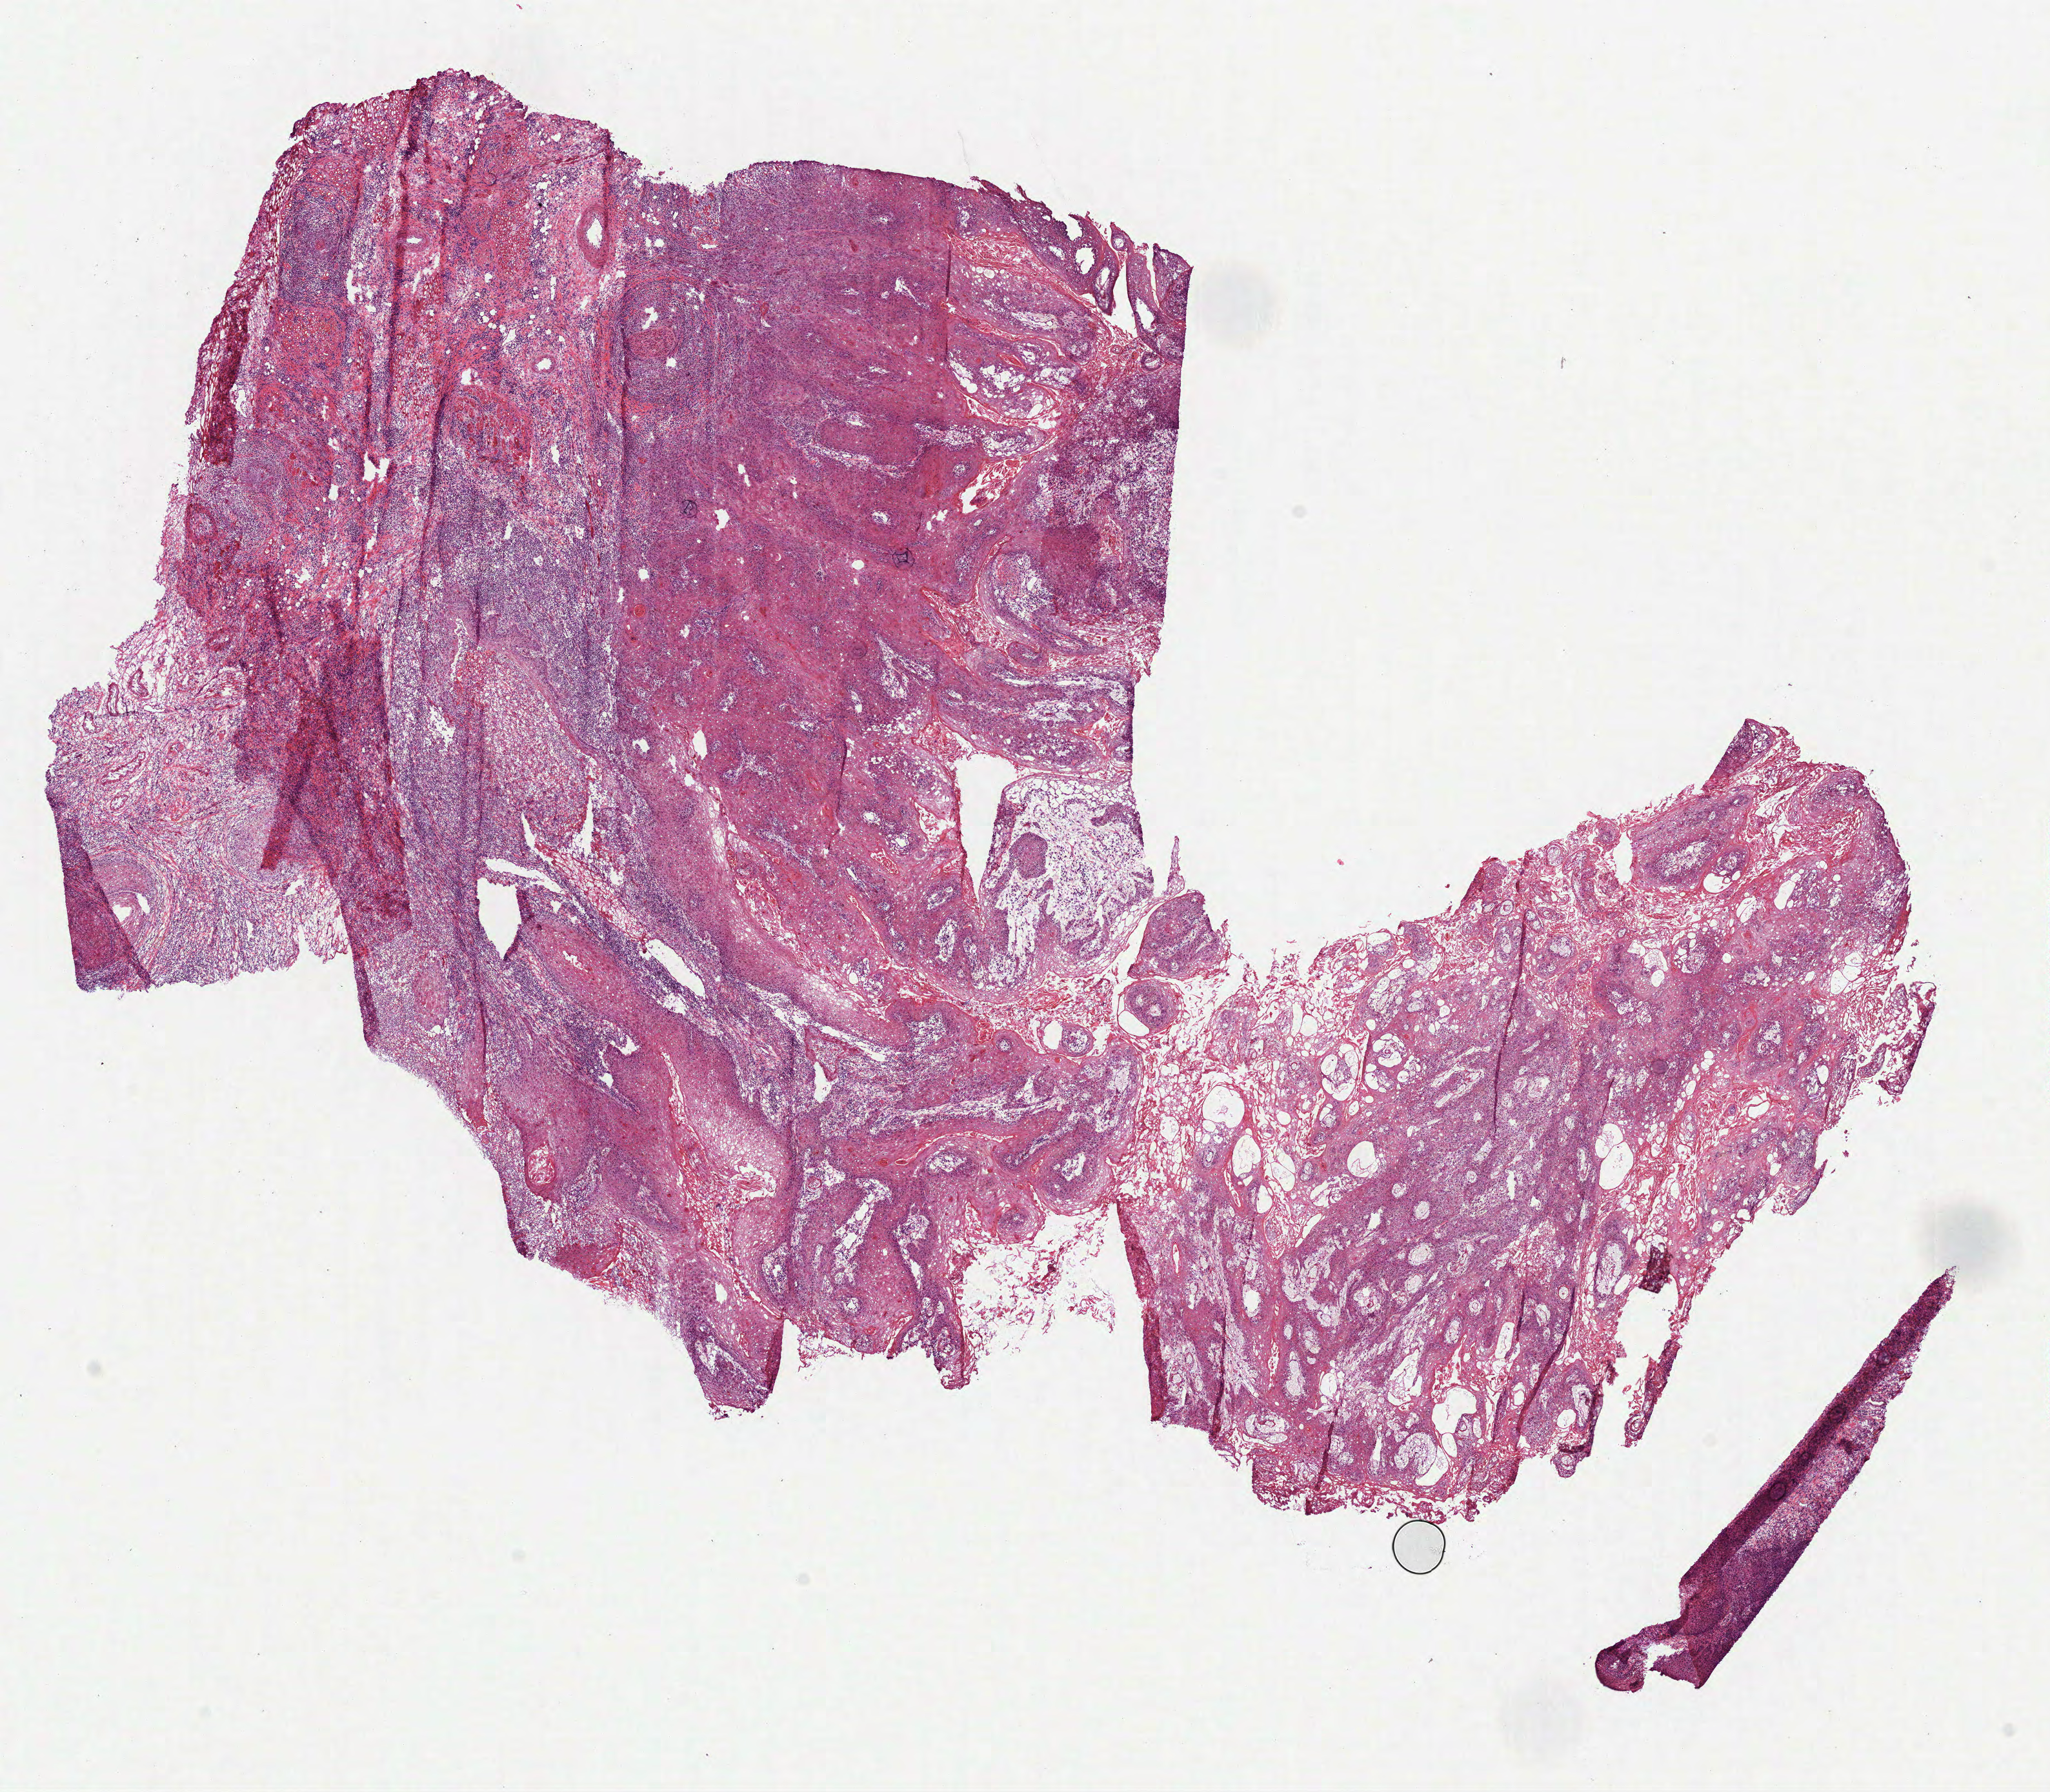
Whole-slide histology image, H&E, whole scanned area (about 12.8 x 11.2 mm, from a 40x scan) shown as a low-resolution overview. Frozen section. Head and neck, primary tumour sample. Patient: female, age at initial diagnosis 77 years. Histologic grade: G2 (moderately differentiated). Composition of this section per pathologist review: tumour cells 80%, tumour nuclei 60%, normal cells 13%, stromal cells 7%, necrosis 0%. Infiltration values recorded for this section: lymphocyte infiltration 15%, monocyte infiltration 0%, neutrophil infiltration 10%.
AJCC pathologic stage: I (7th edition). Histologic diagnosis: Squamous cell carcinoma, NOS (tongue, NOS). Lymph nodes positive (case pathology): 0 of 25 examined.